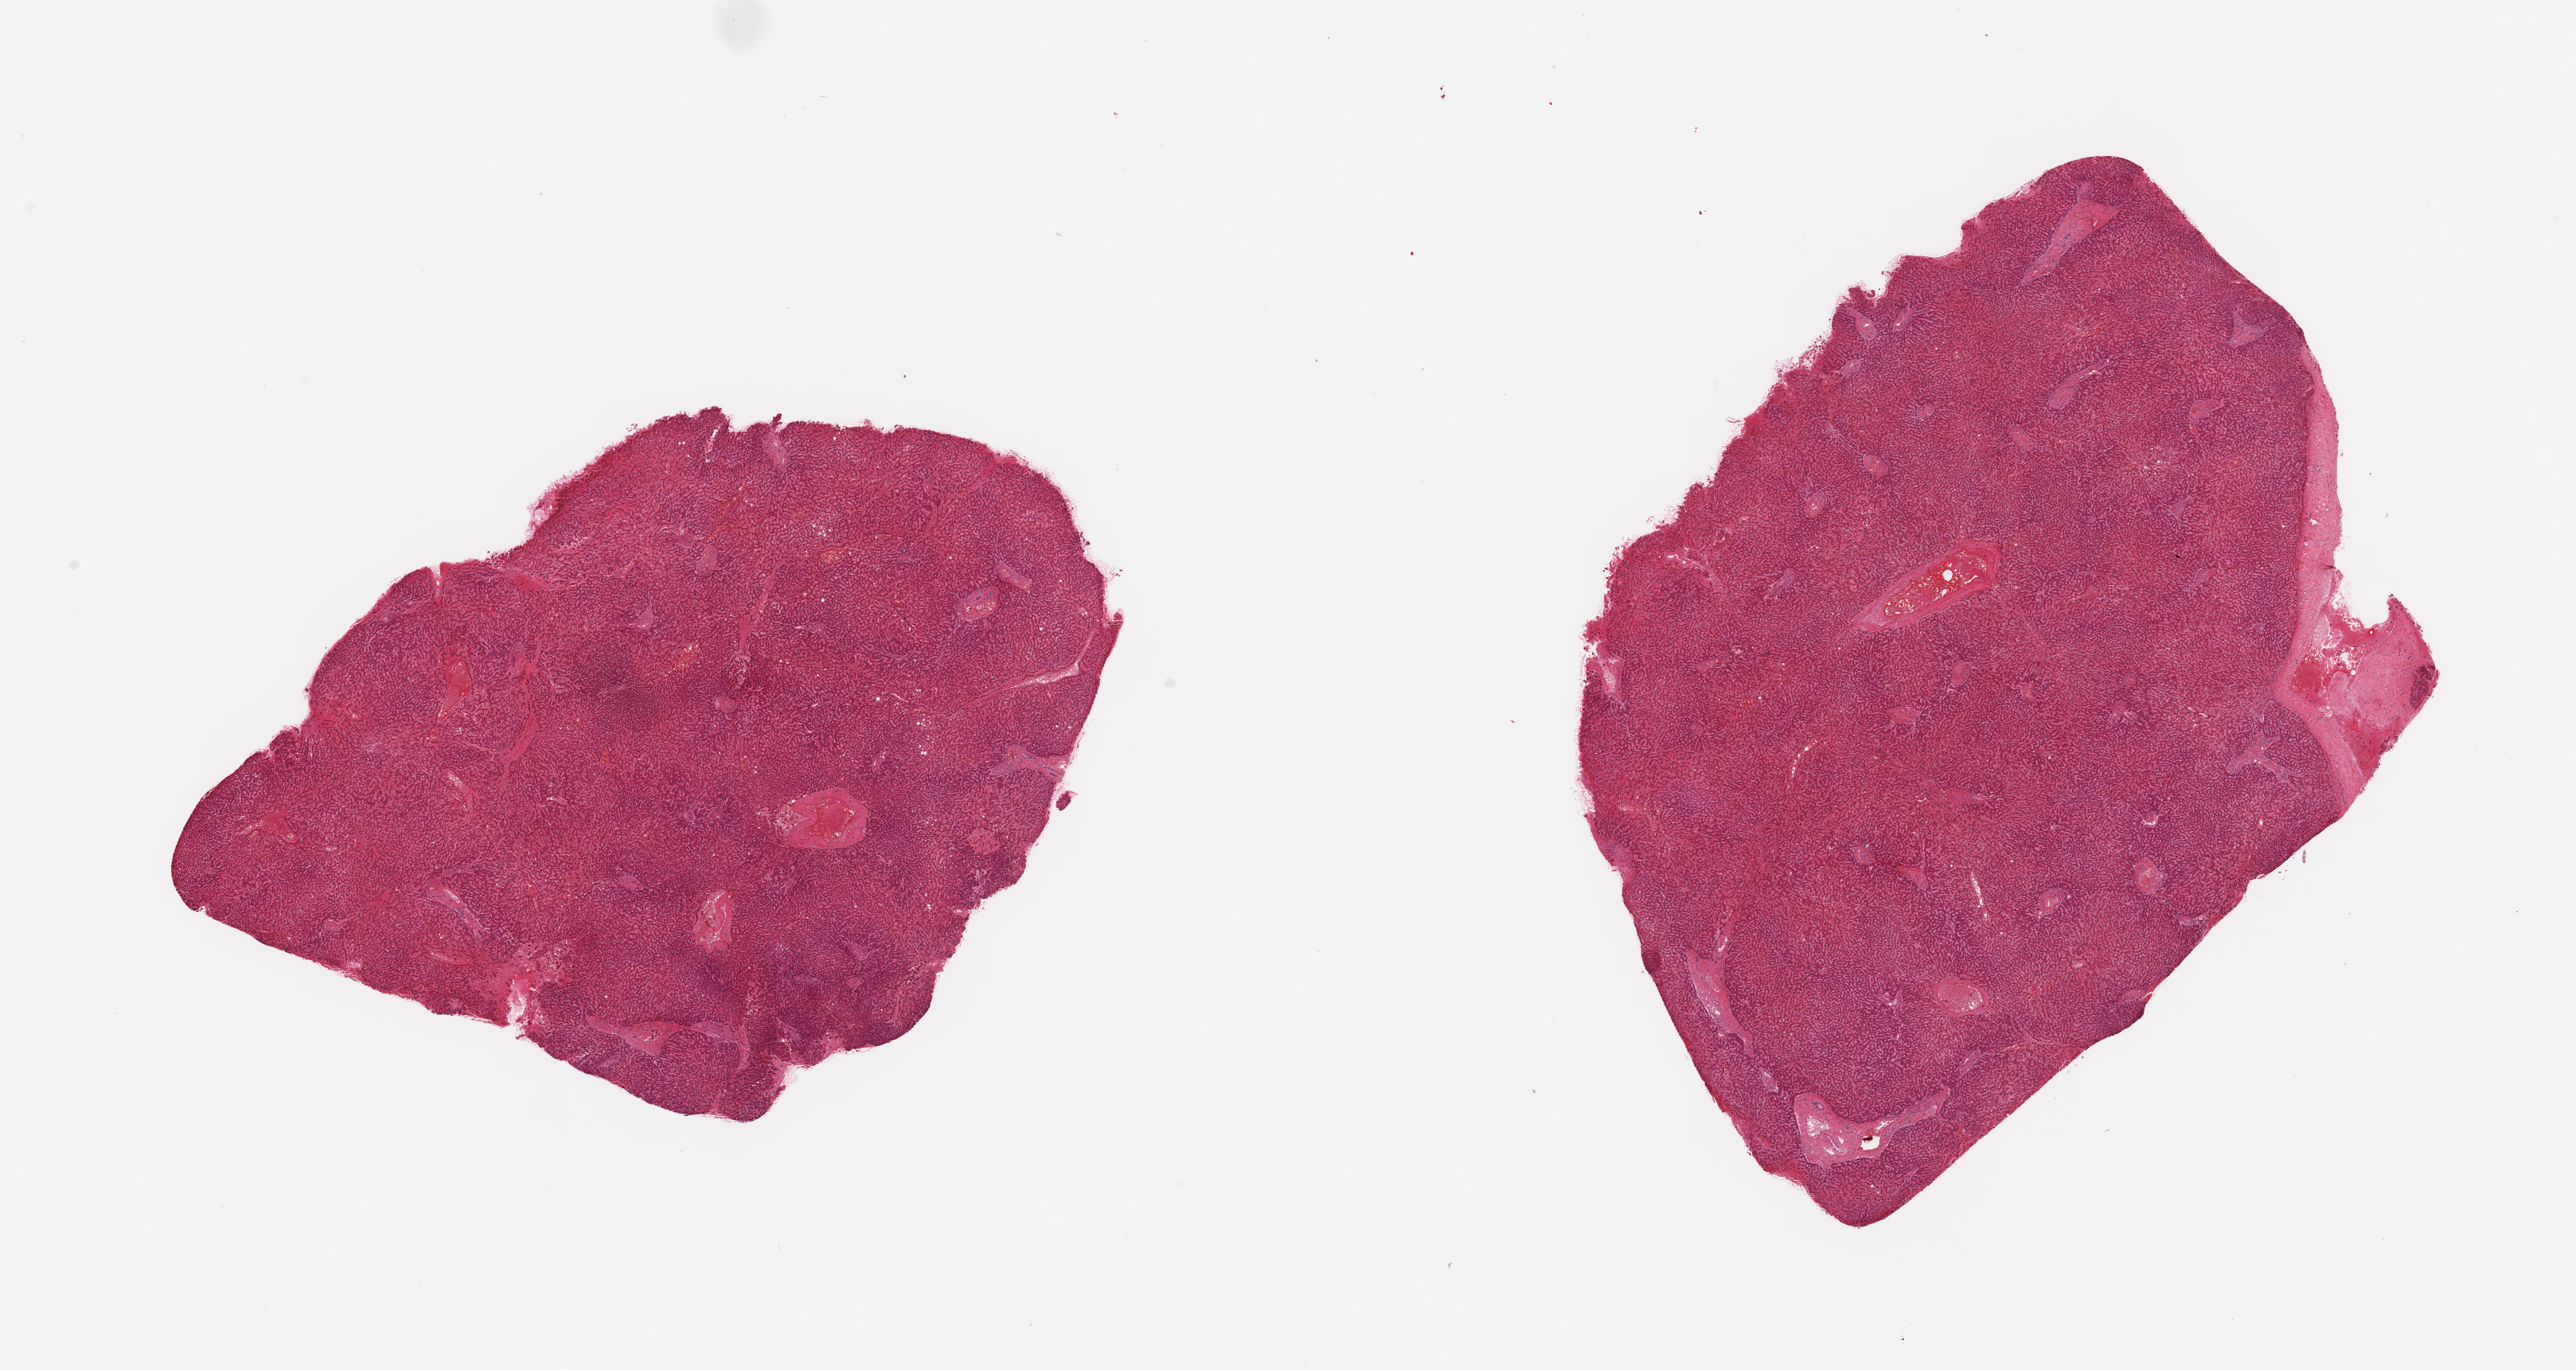
Haematoxylin and eosin whole-slide image, a low-resolution overview of the entire scanned area, about 25.6 x 13.6 mm (from a 20x scan); PAXgene-fixed paraffin-embedded (PFPE) section; section of liver (target tissue); donor tissue sample. Donor sex: male.
Review note (as recorded): 2 pieces; congested; large vein on 1 edge.